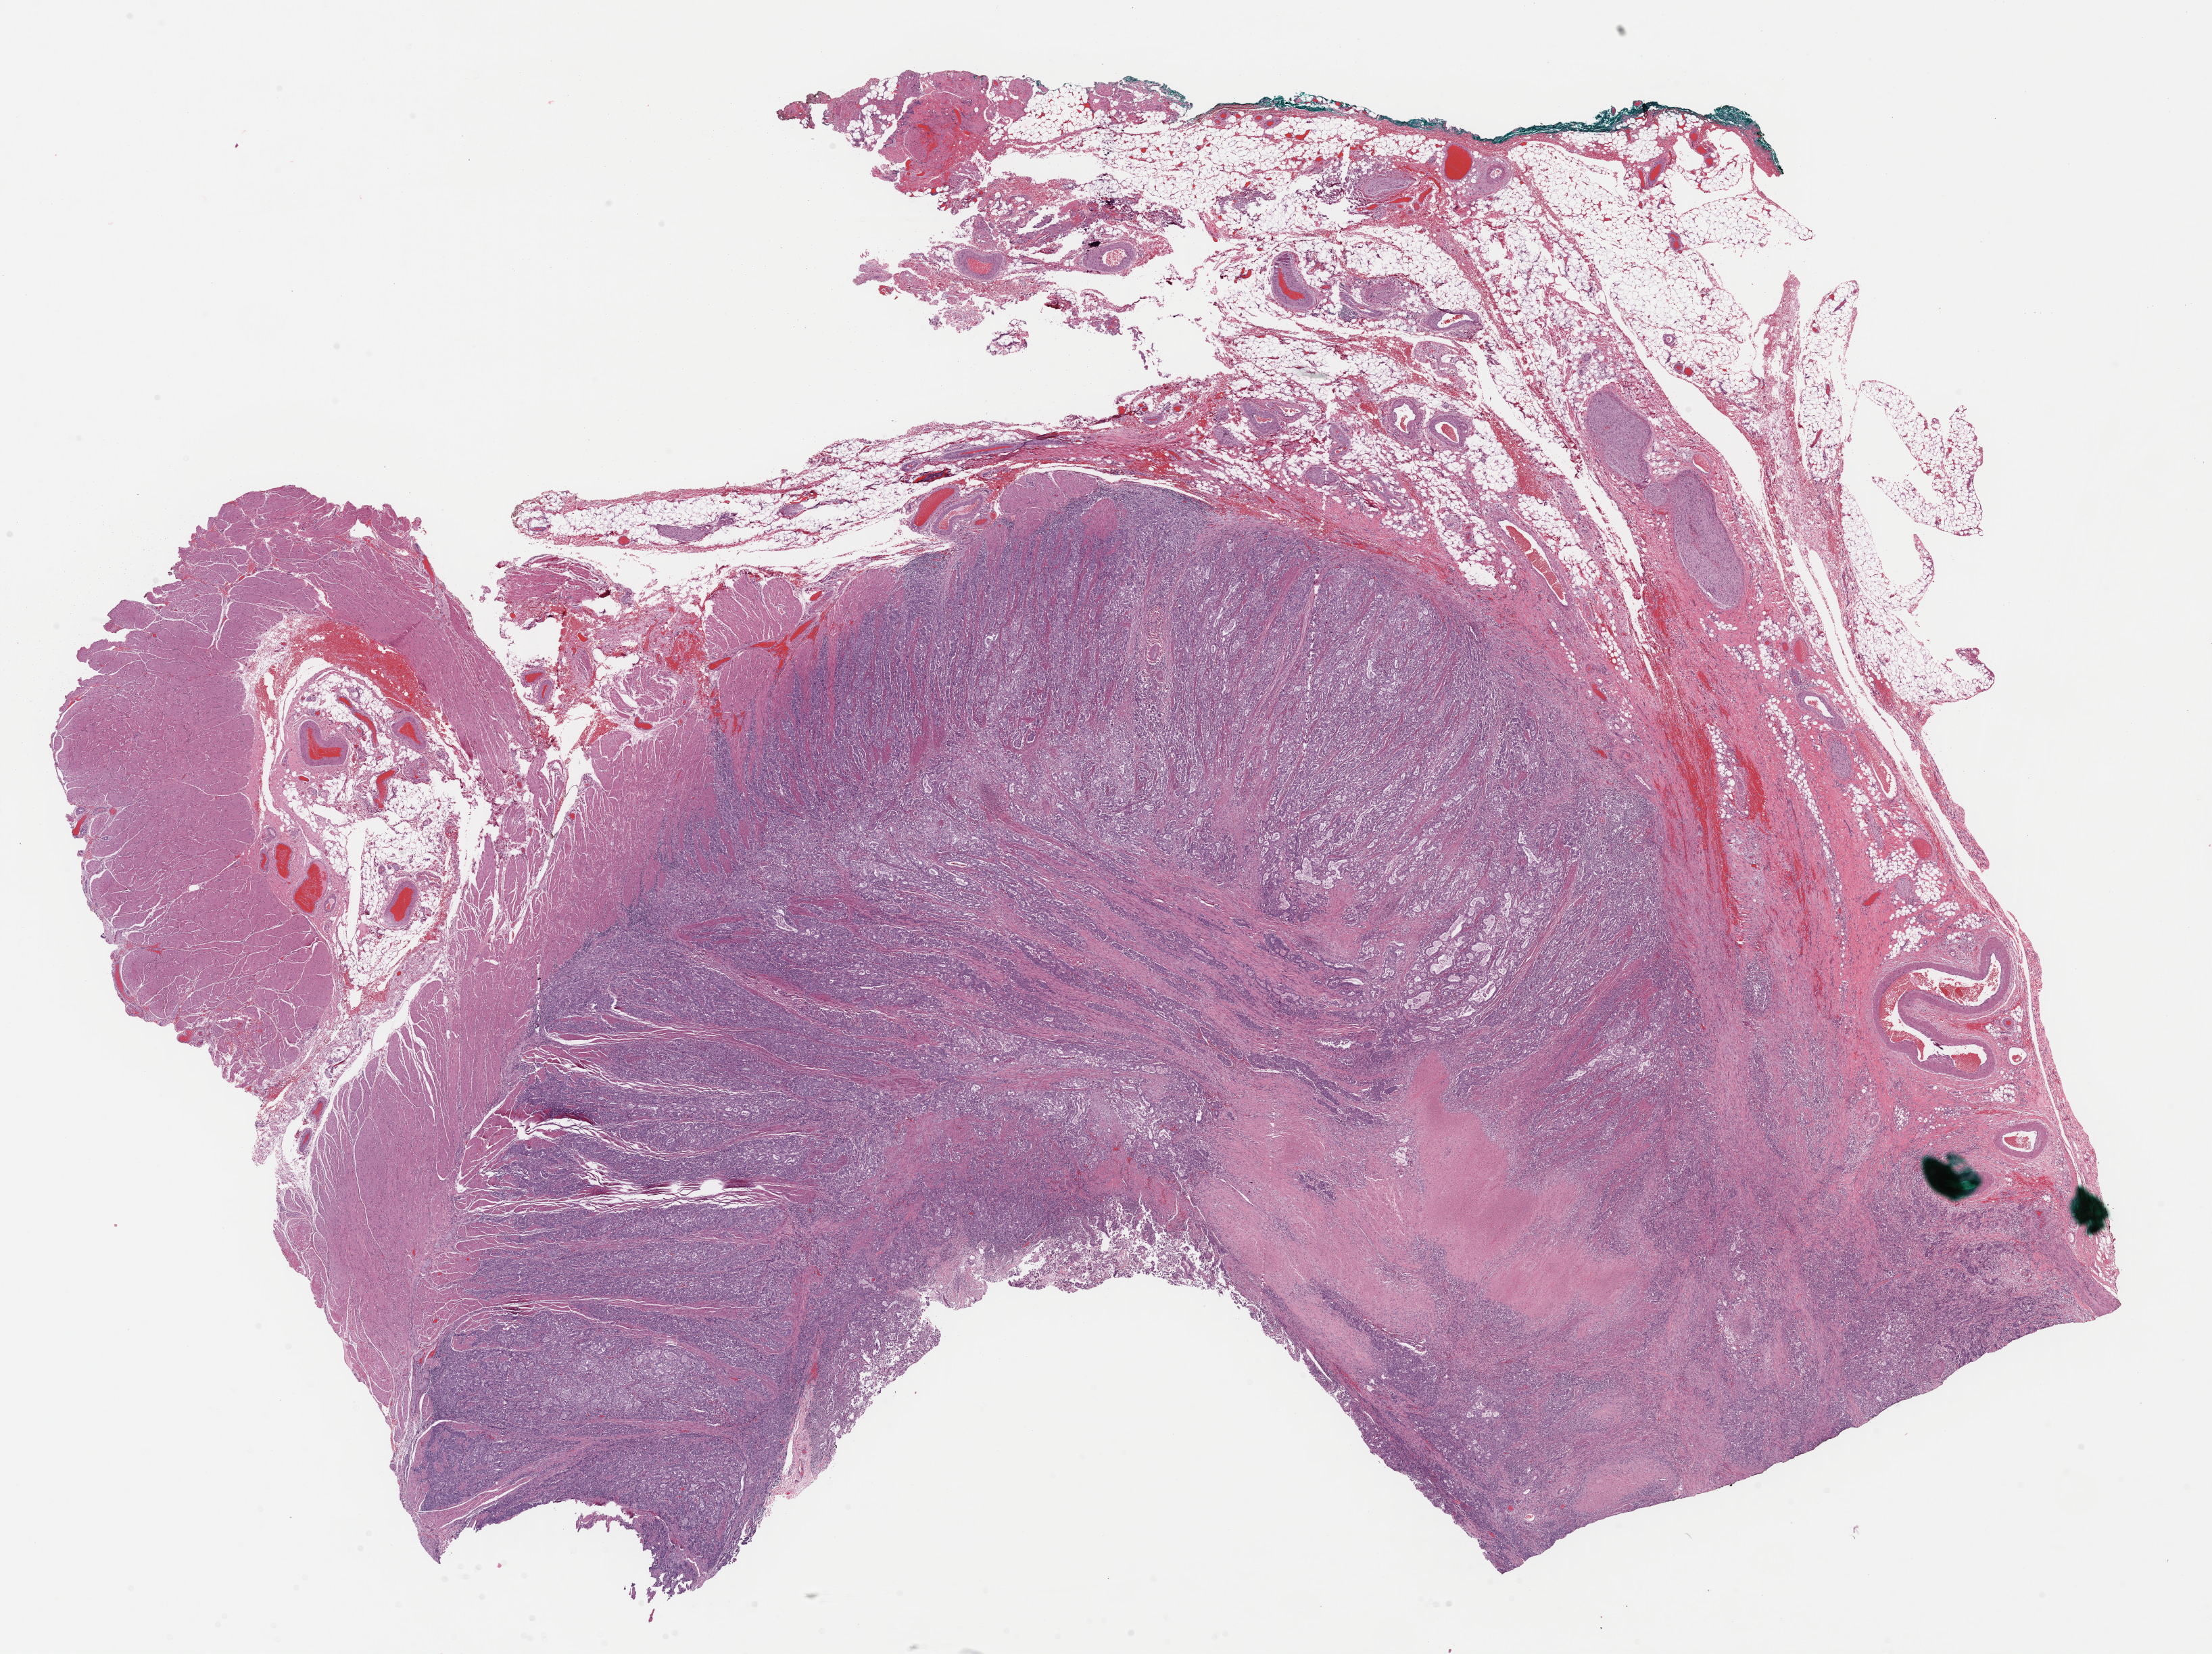
H&E-stained whole-slide image — low-resolution overview of the scanned area, about 25.8 x 19.3 mm (acquisition: 40x scan). FFPE section. Primary tumour sample from the esophagus. Male, age 81 years at initial diagnosis. Histologic grade: GX (grade cannot be assessed).
- AJCC pathologic stage: IIA (6th edition)
- histologic diagnosis: Adenocarcinoma, NOS (lower third of esophagus)
- lymph nodes positive (case pathology): 0 of 12 examined